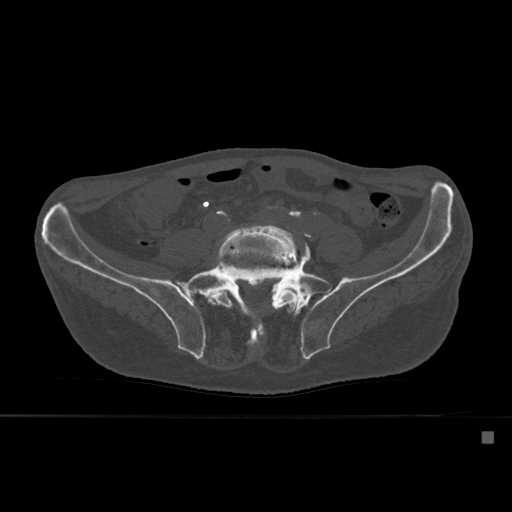
CT including the spine, one axial slice; bone window (W 1800 / L 400 HU); 512 × 512 image matrix. Male patient, age 78 years. Case-level facts recorded for this patient, not image findings: primary cancer: prostate.
Annotated regions visible in this slice (semi-automatically segmented with operator editing):
- L5 vertebra: box from (x=207, y=227) to (x=300, y=347) px